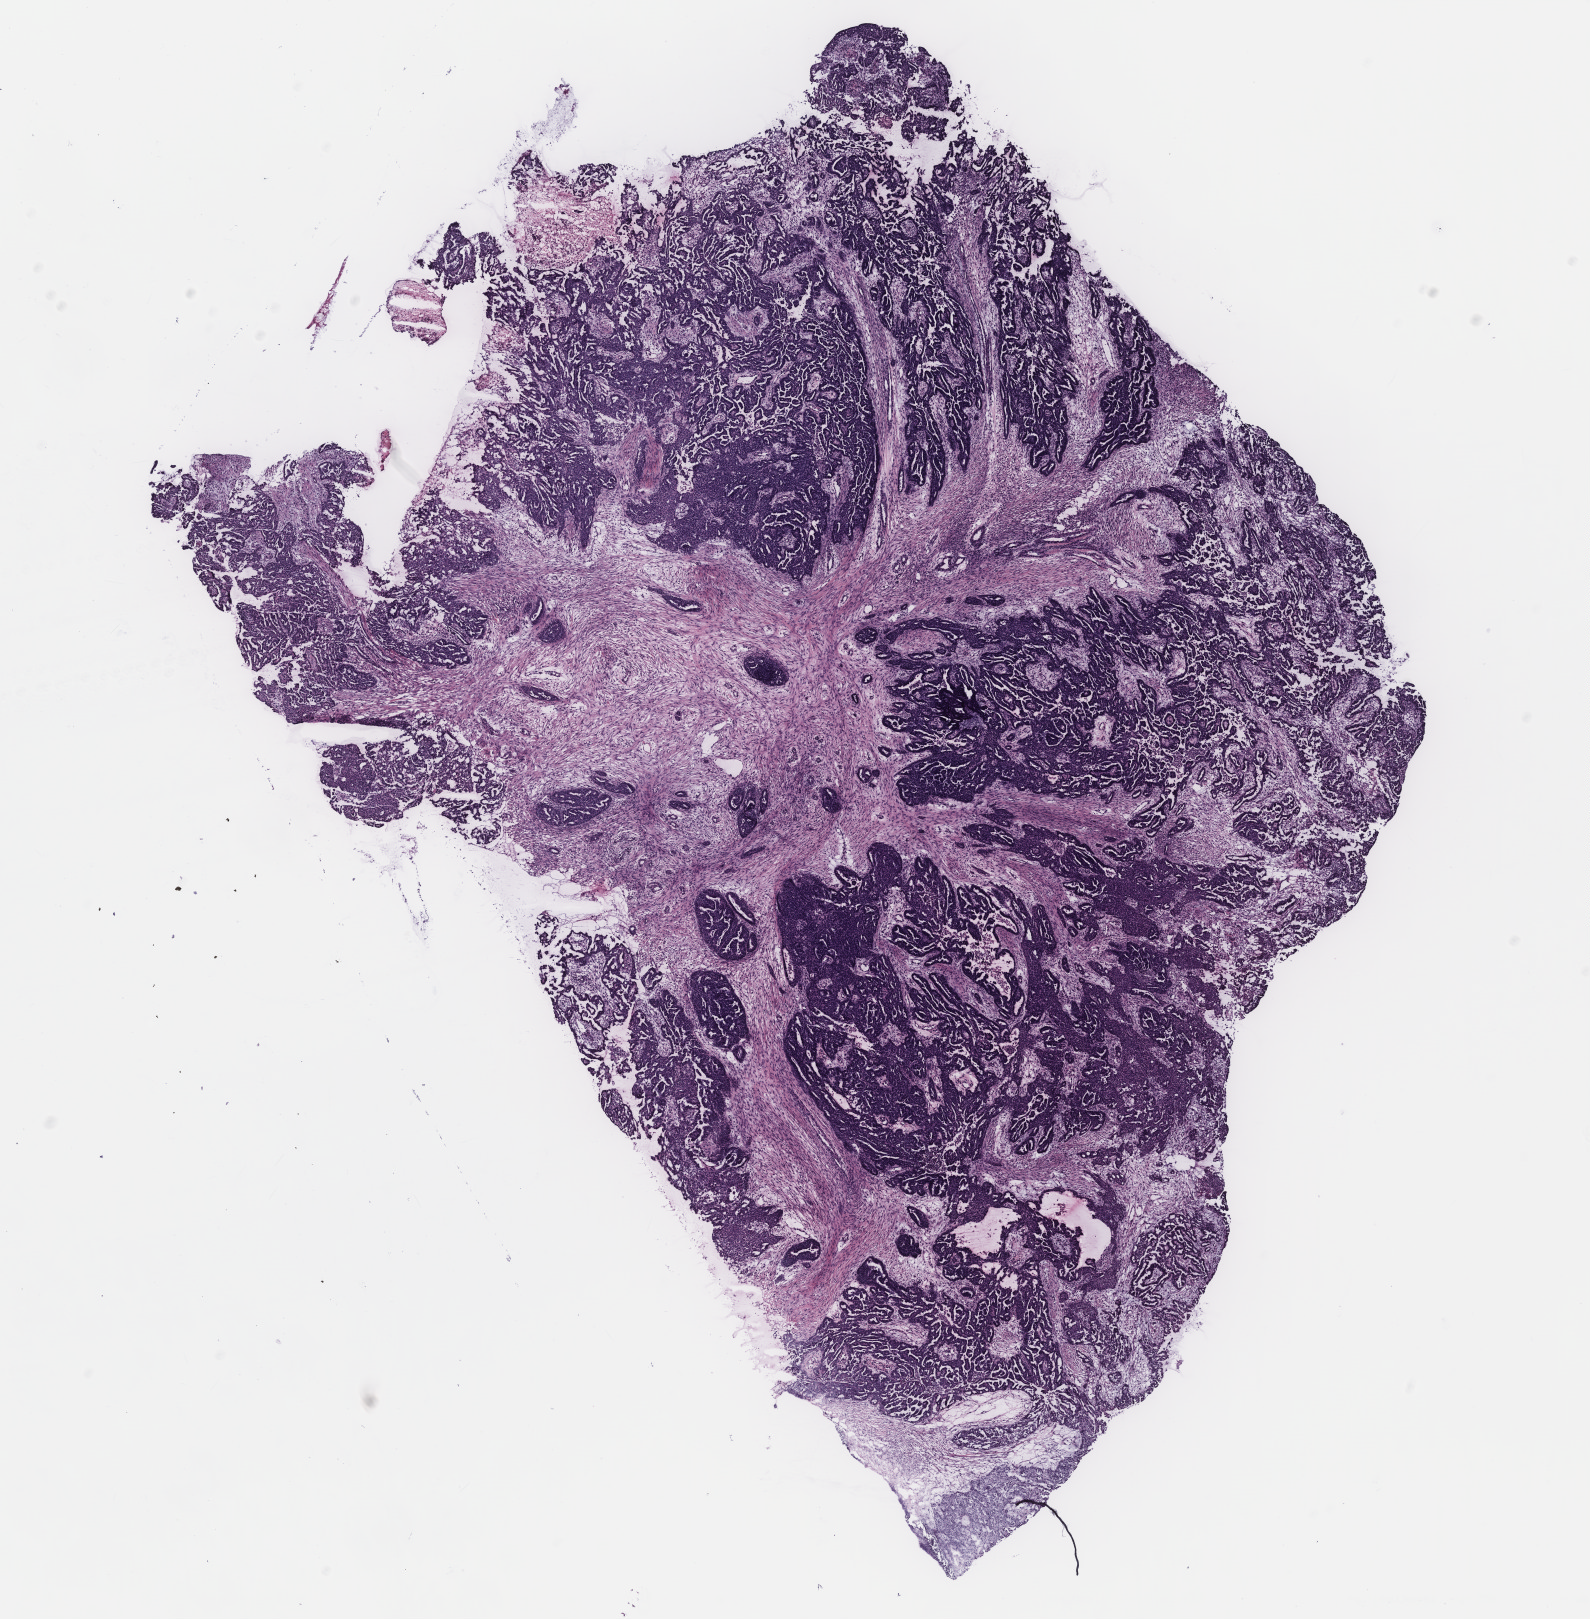
Hematoxylin and eosin (H&E) stained whole-slide image, whole scanned area (about 12.7 x 13.0 mm, acquisition: 40x scan) shown as a low-resolution overview. Ovary, tumour tissue. 50-year-old female patient.
• histologic diagnosis: Serous adenocarcinoma, NOS
• primary tumour site (as recorded): ovary